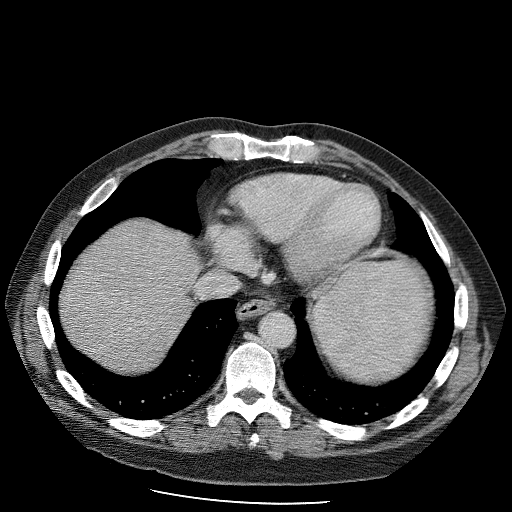
Contrast-enhanced abdominal CT (liver protocol), one axial slice; slice 92 of 98 in the series (ordered by position); reconstruction kernel STANDARD; soft-tissue window (W 400 / L 40 HU); 2.5 mm slice thickness; 512 × 512 image matrix. Case-level facts recorded for this patient, not image findings: diagnosis: hepatocellular carcinoma (patient treated with transarterial chemoembolisation; whether this scan precedes or follows treatment is not stated here); TNM stage (as recorded): Stage-II; Child-Pugh class: B; tumour differentiation: moderately differentiated; tumour nodularity: uninodular.
Annotated regions visible in this slice (semi-automatic segmentation, software-assisted and operator-edited):
- liver parenchyma outside the tumour (the mass and vessels are separate outlines, so this box may not span the whole liver): bounding box [x1, y1, x2, y2] px = [64, 218, 200, 364]